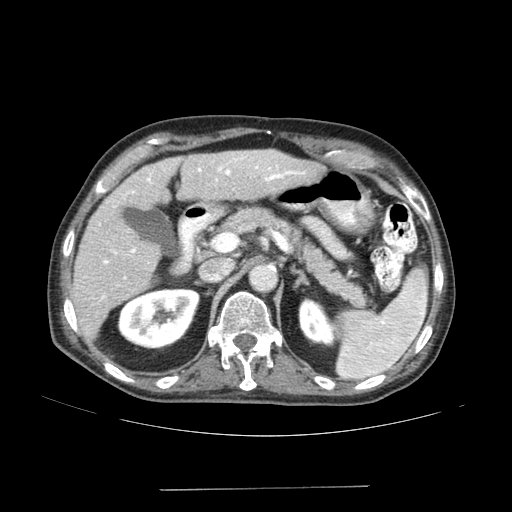
Contrast-enhanced abdominal CT (liver protocol), one axial slice; slice 90 of 192 in the series (ordered by position); 120 kVp; soft-tissue window (W 400 / L 40 HU); 2.5 mm slice thickness; 512 × 512 image matrix. From the clinical record (not read from this slice): diagnosis: hepatocellular carcinoma (patient treated with transarterial chemoembolisation; whether this scan precedes or follows treatment is not stated here); TNM stage (as recorded): Stage-IVA; Child-Pugh class: A.
Outlined on this slice (semi-automatic segmentation, software-assisted and operator-edited):
- liver parenchyma outside the tumour (the mass and vessels are separate outlines, so this box may not span the whole liver): bounding box [x1, y1, x2, y2] px = [70, 150, 323, 340]
- liver vessels: [102, 157, 304, 299]